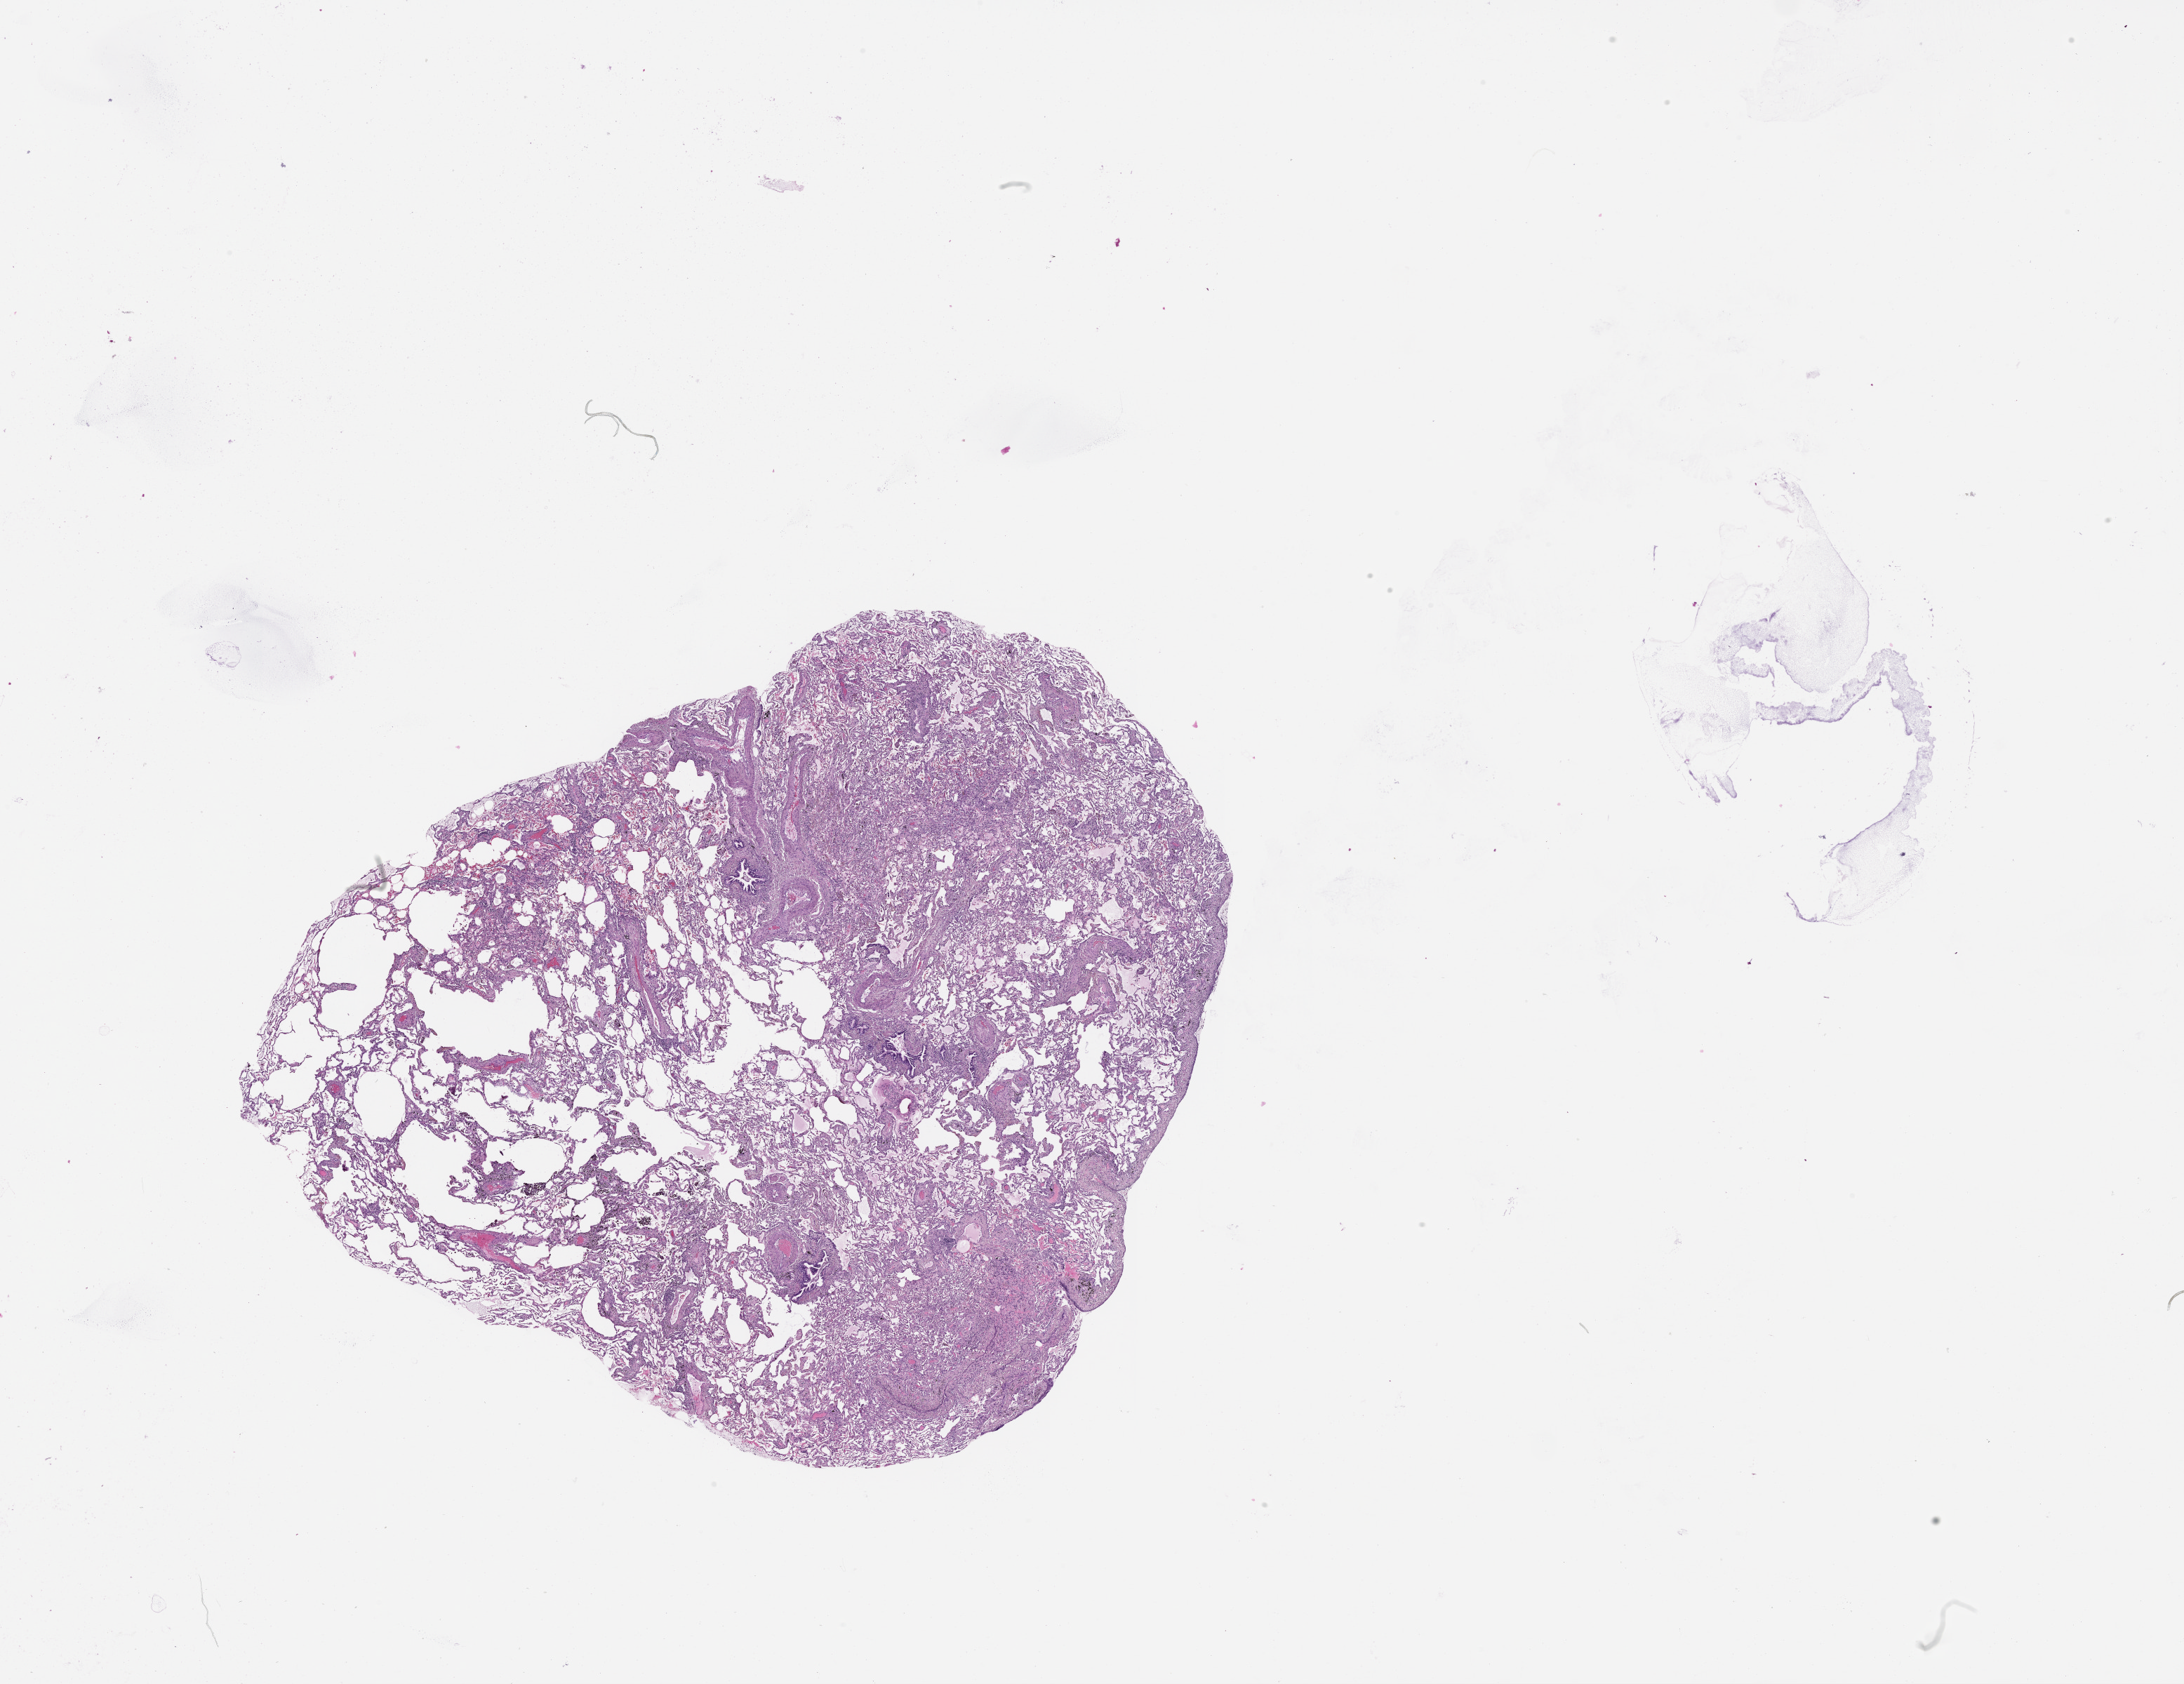
H&E-stained whole-slide image, low-resolution overview of the scanned area, about 25.1 x 19.3 mm (acquisition: 20x scan). Lung, tissue type not recorded.
Patient diagnosis (cohort enrolment): squamous cell carcinoma (lung).